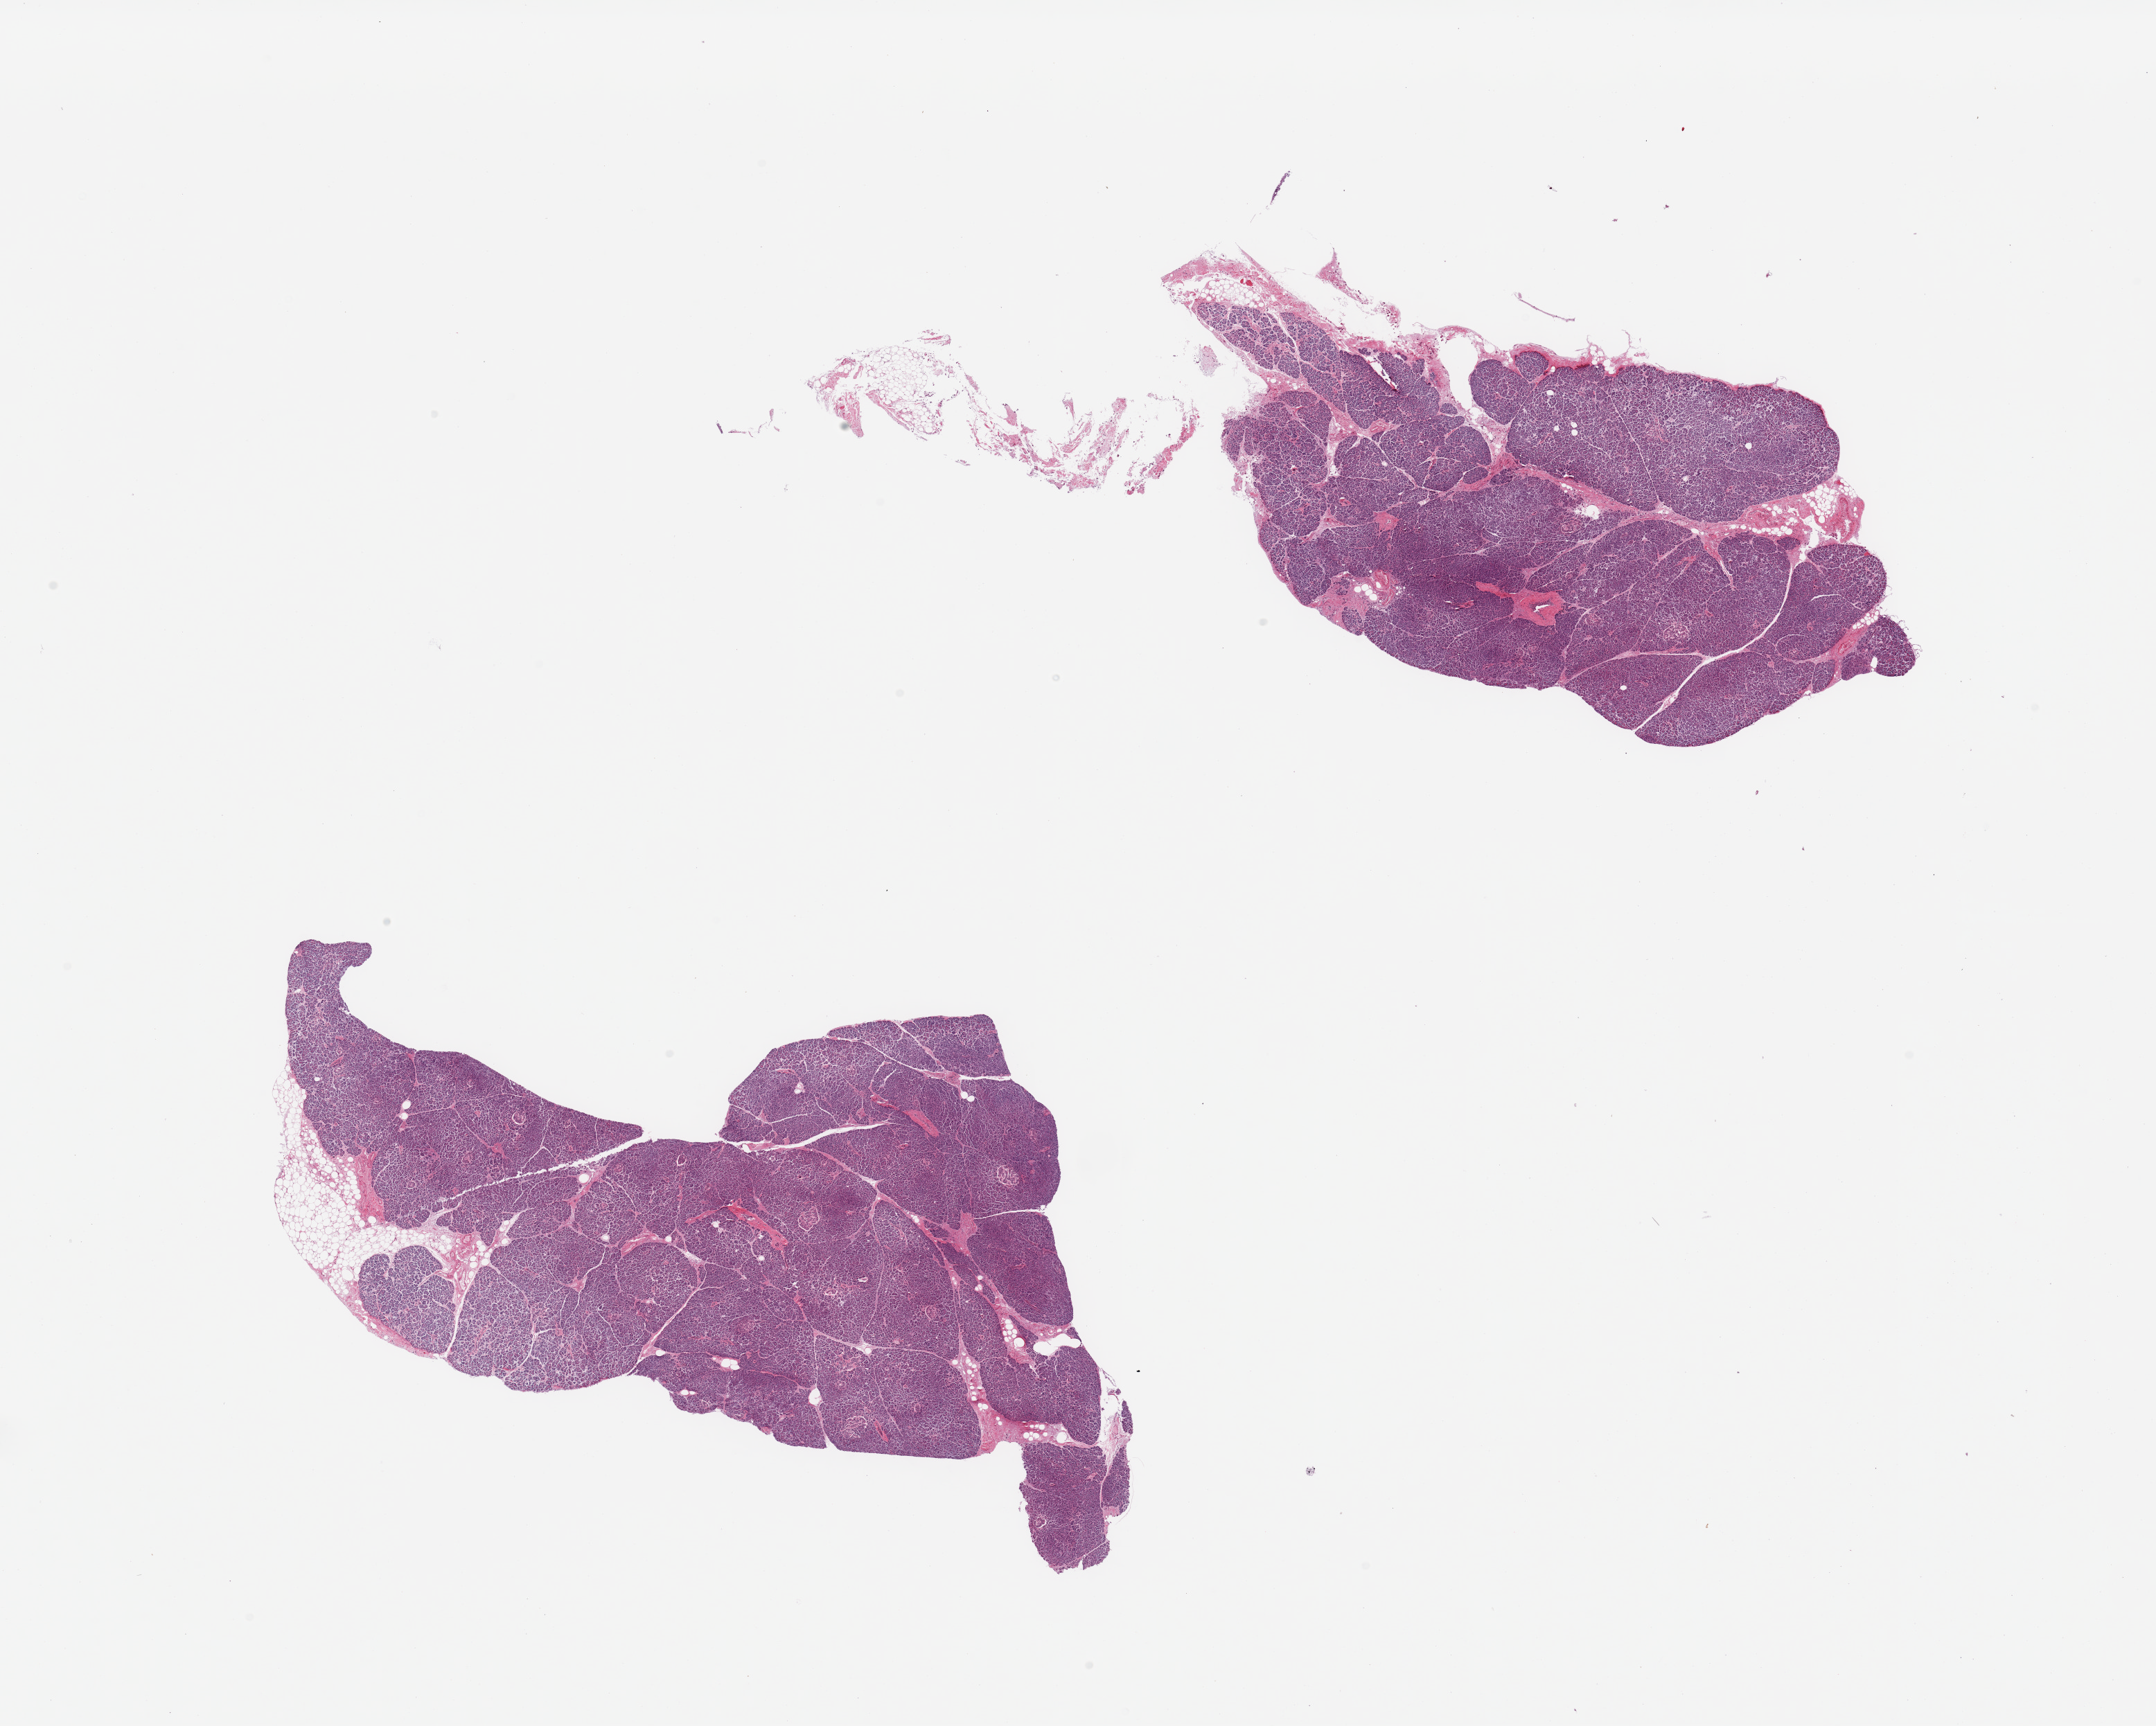
Haematoxylin and eosin whole-slide image, brightfield, a low-resolution overview of the entire scanned area, about 24.6 x 19.7 mm, PAXgene-fixed, paraffin-embedded tissue, sampled site (target tissue): pancreas, donor tissue sample. Male donor.
Reviewer comment on this tissue sample: 2 pieces; small amount of external fat; minimal internal fat.